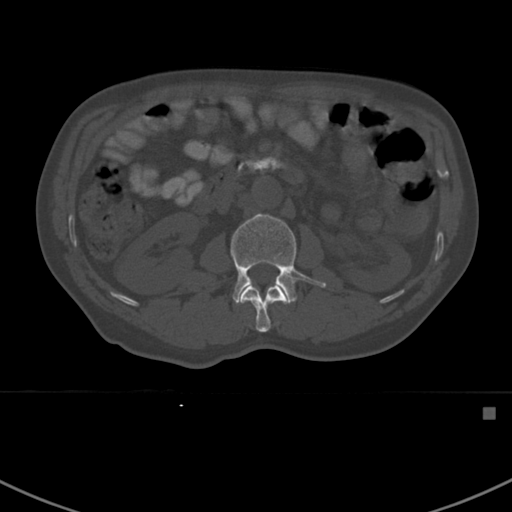
CT including the spine, one axial slice. Slice 295 of 412 in the series (ordered by position). Reconstruction kernel Br40s. 120 kVp. Bone window (W 1800 / L 400 HU). 1.5 mm slice thickness. 512 × 512 image matrix. Male patient, age 59 years. Case-level facts recorded for this patient, not image findings: primary cancer: prostate.
Structures marked on this image (semi-automatic segmentation, software-assisted and operator-edited):
- L1 vertebra: bounding box [x1, y1, x2, y2] px = [240, 285, 288, 332]
- L2 vertebra: [230, 214, 326, 304]